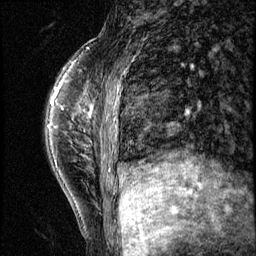
Breast MRI (dynamic contrast-enhanced), one sagittal slice; position 16 of 56 along the scan axis; 3 images stored at this slice position (order not interpretable as contrast timing); 1.5 T; TE 4.2 ms, TR 8.7 ms; 2.5 mm slice thickness; 256 × 256 image matrix. Female patient, age 35 years. From the clinical record (not read from this slice): setting: breast cancer imaged before/during neoadjuvant chemotherapy; receptor status: HER2-positive.
Structures marked on this image (semi-automatically segmented with operator editing):
- analysis volume of interest (the breast-tissue region the enhancement analysis was run in; not a lesion): box from (x=58, y=84) to (x=138, y=186) px
- tumour enhancement mask (voxels above the 140 % enhancement threshold inside the analysis volume of interest): (x=88, y=111)–(x=110, y=171)